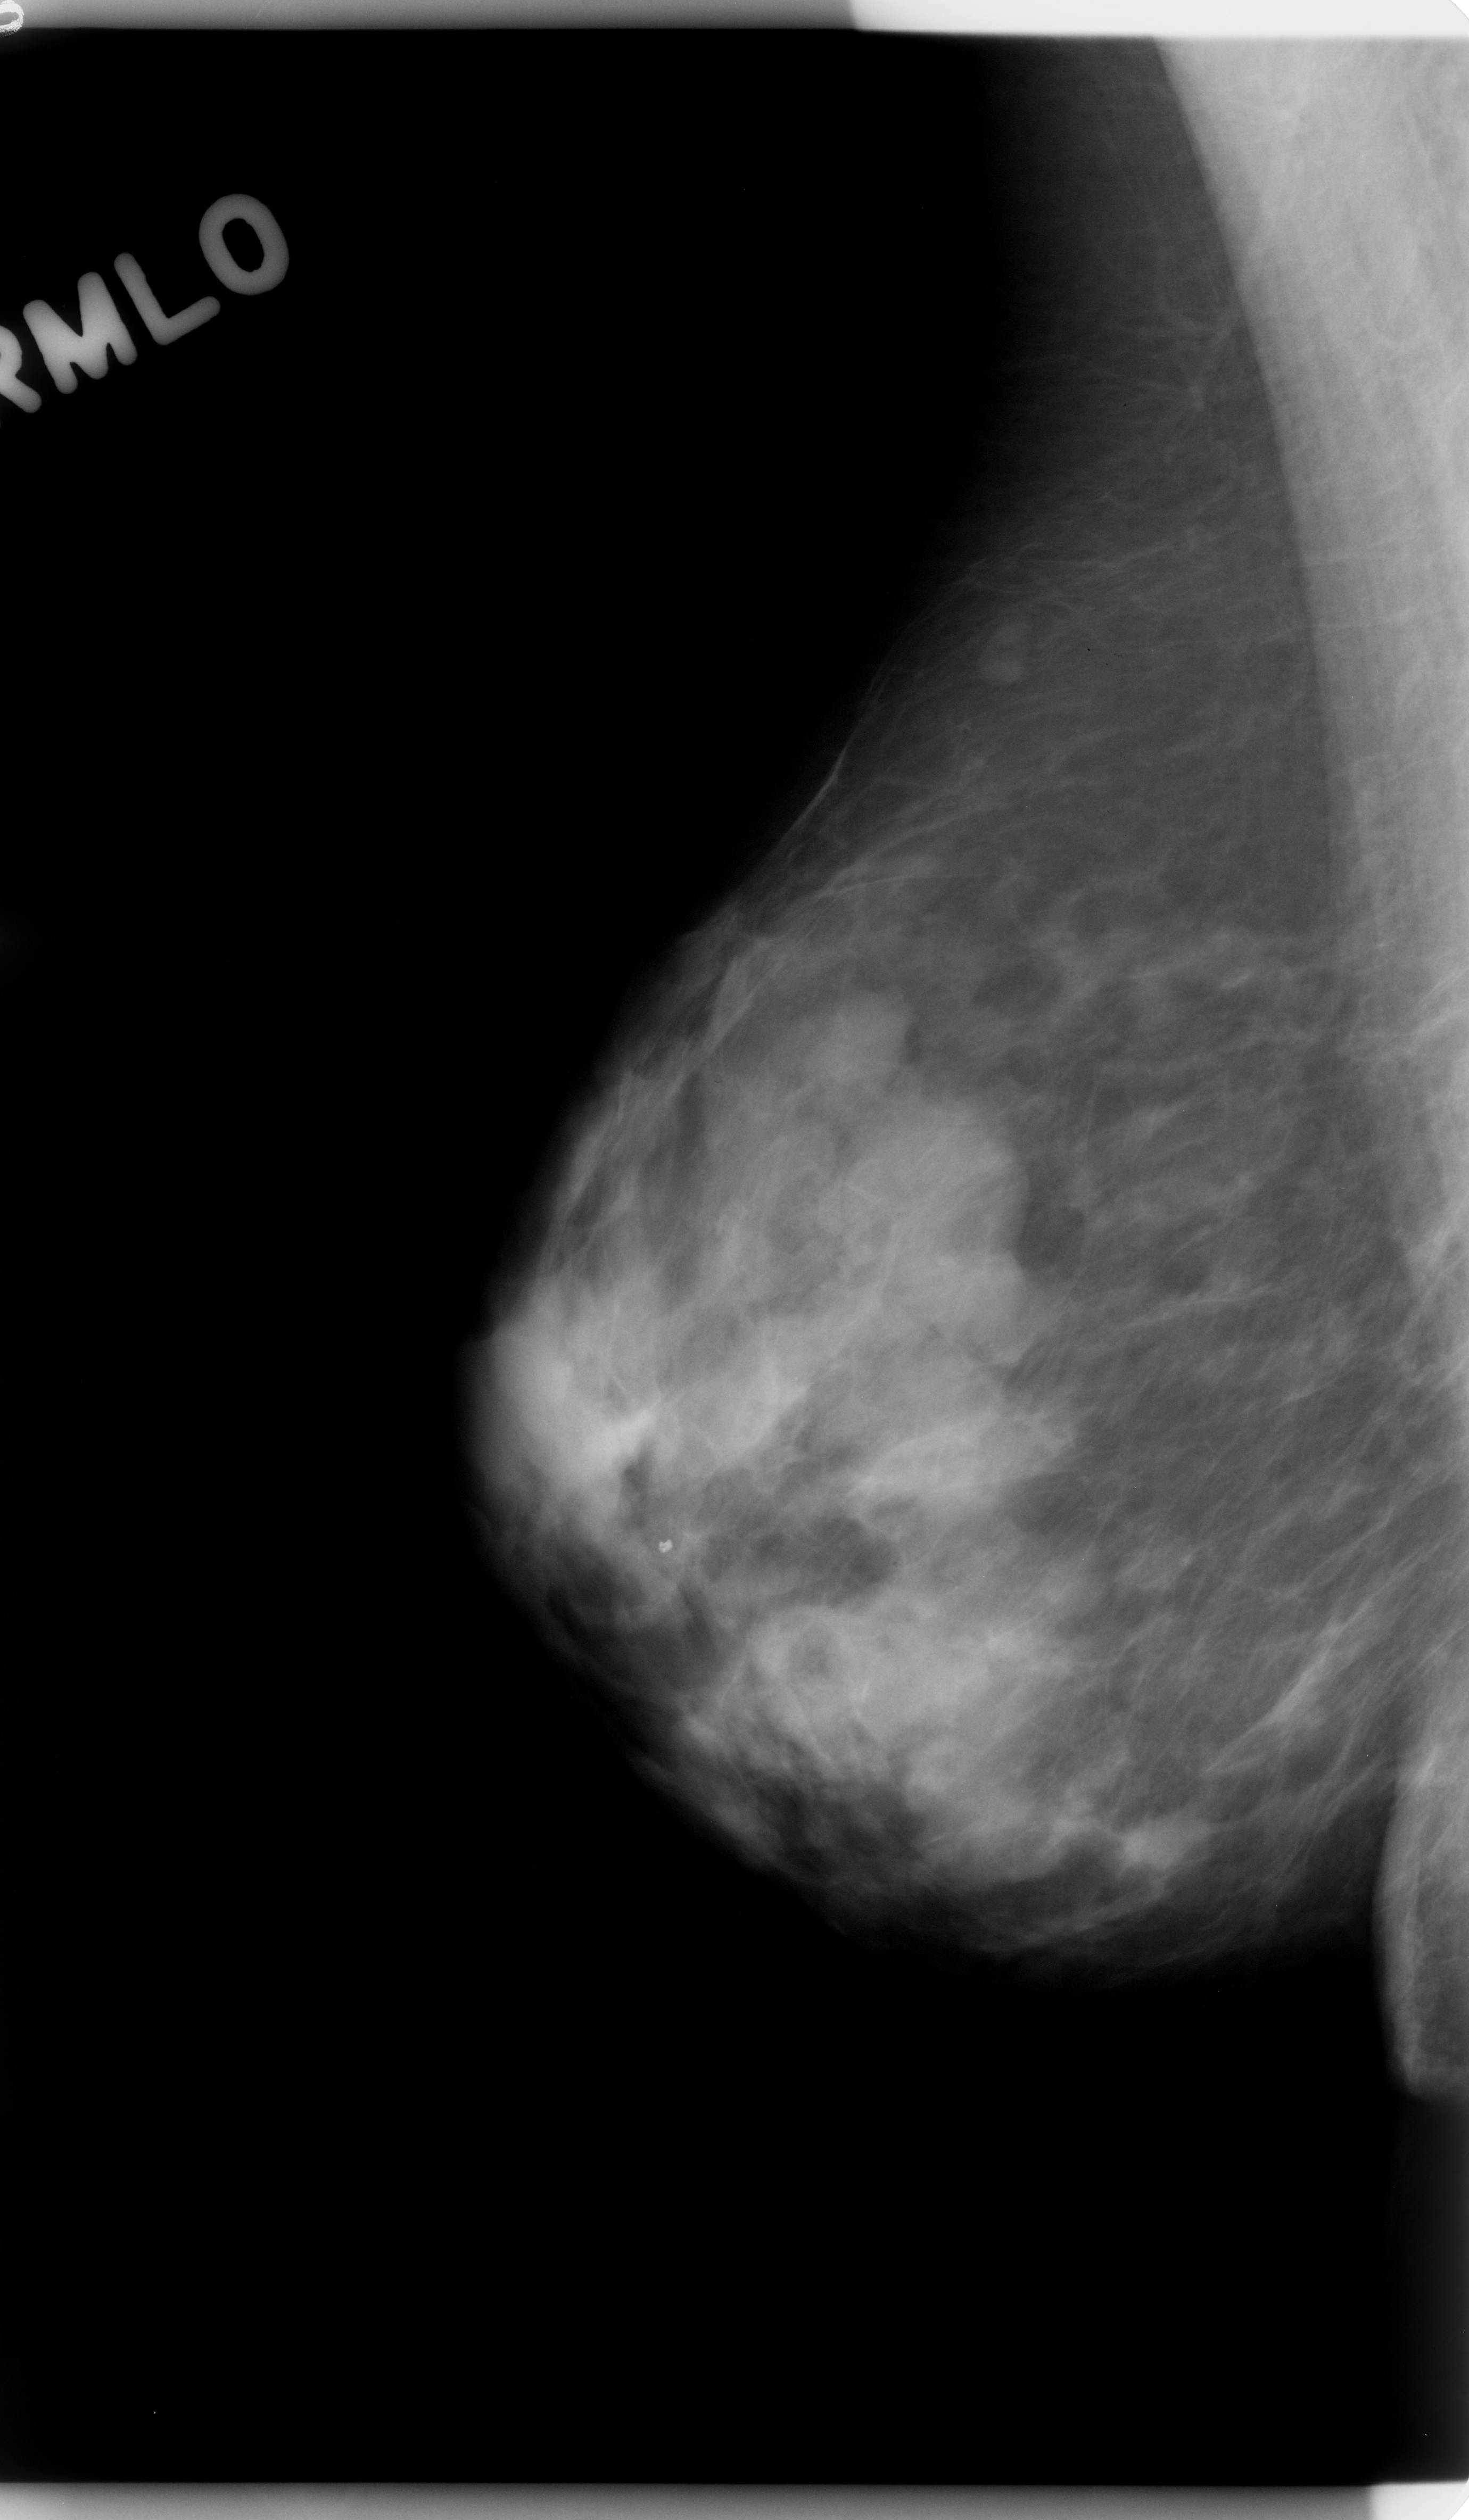
Scanned film-screen mammogram; right breast; MLO view.
Marked findings (only marked abnormalities are described; nothing is implied about the rest of the image): mass, shape lobulated, margins circumscribed; BI-RADS assessment category 3; subtlety rating 4 on a 1 (subtle) to 5 (obvious) scale; pathology (as recorded): benign.